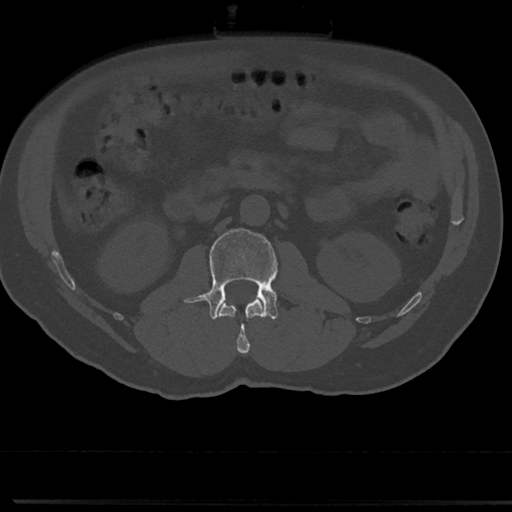
CT including the spine, one axial slice; slice 35 of 817 in the series (ordered by position); reconstruction kernel Br40s/3; 120 kVp; bone window (W 1800 / L 400 HU); 0.5 mm slice thickness; 512 × 512 image matrix. Patient: male, 61 years. From the clinical record (not read from this slice): primary cancer: prostate.
Structures marked on this image (semi-automatically segmented with operator editing):
- L1 vertebra: bounding box <219,299,263,355> (left, top, right, bottom; pixels)
- L2 vertebra: <191,228,278,319>